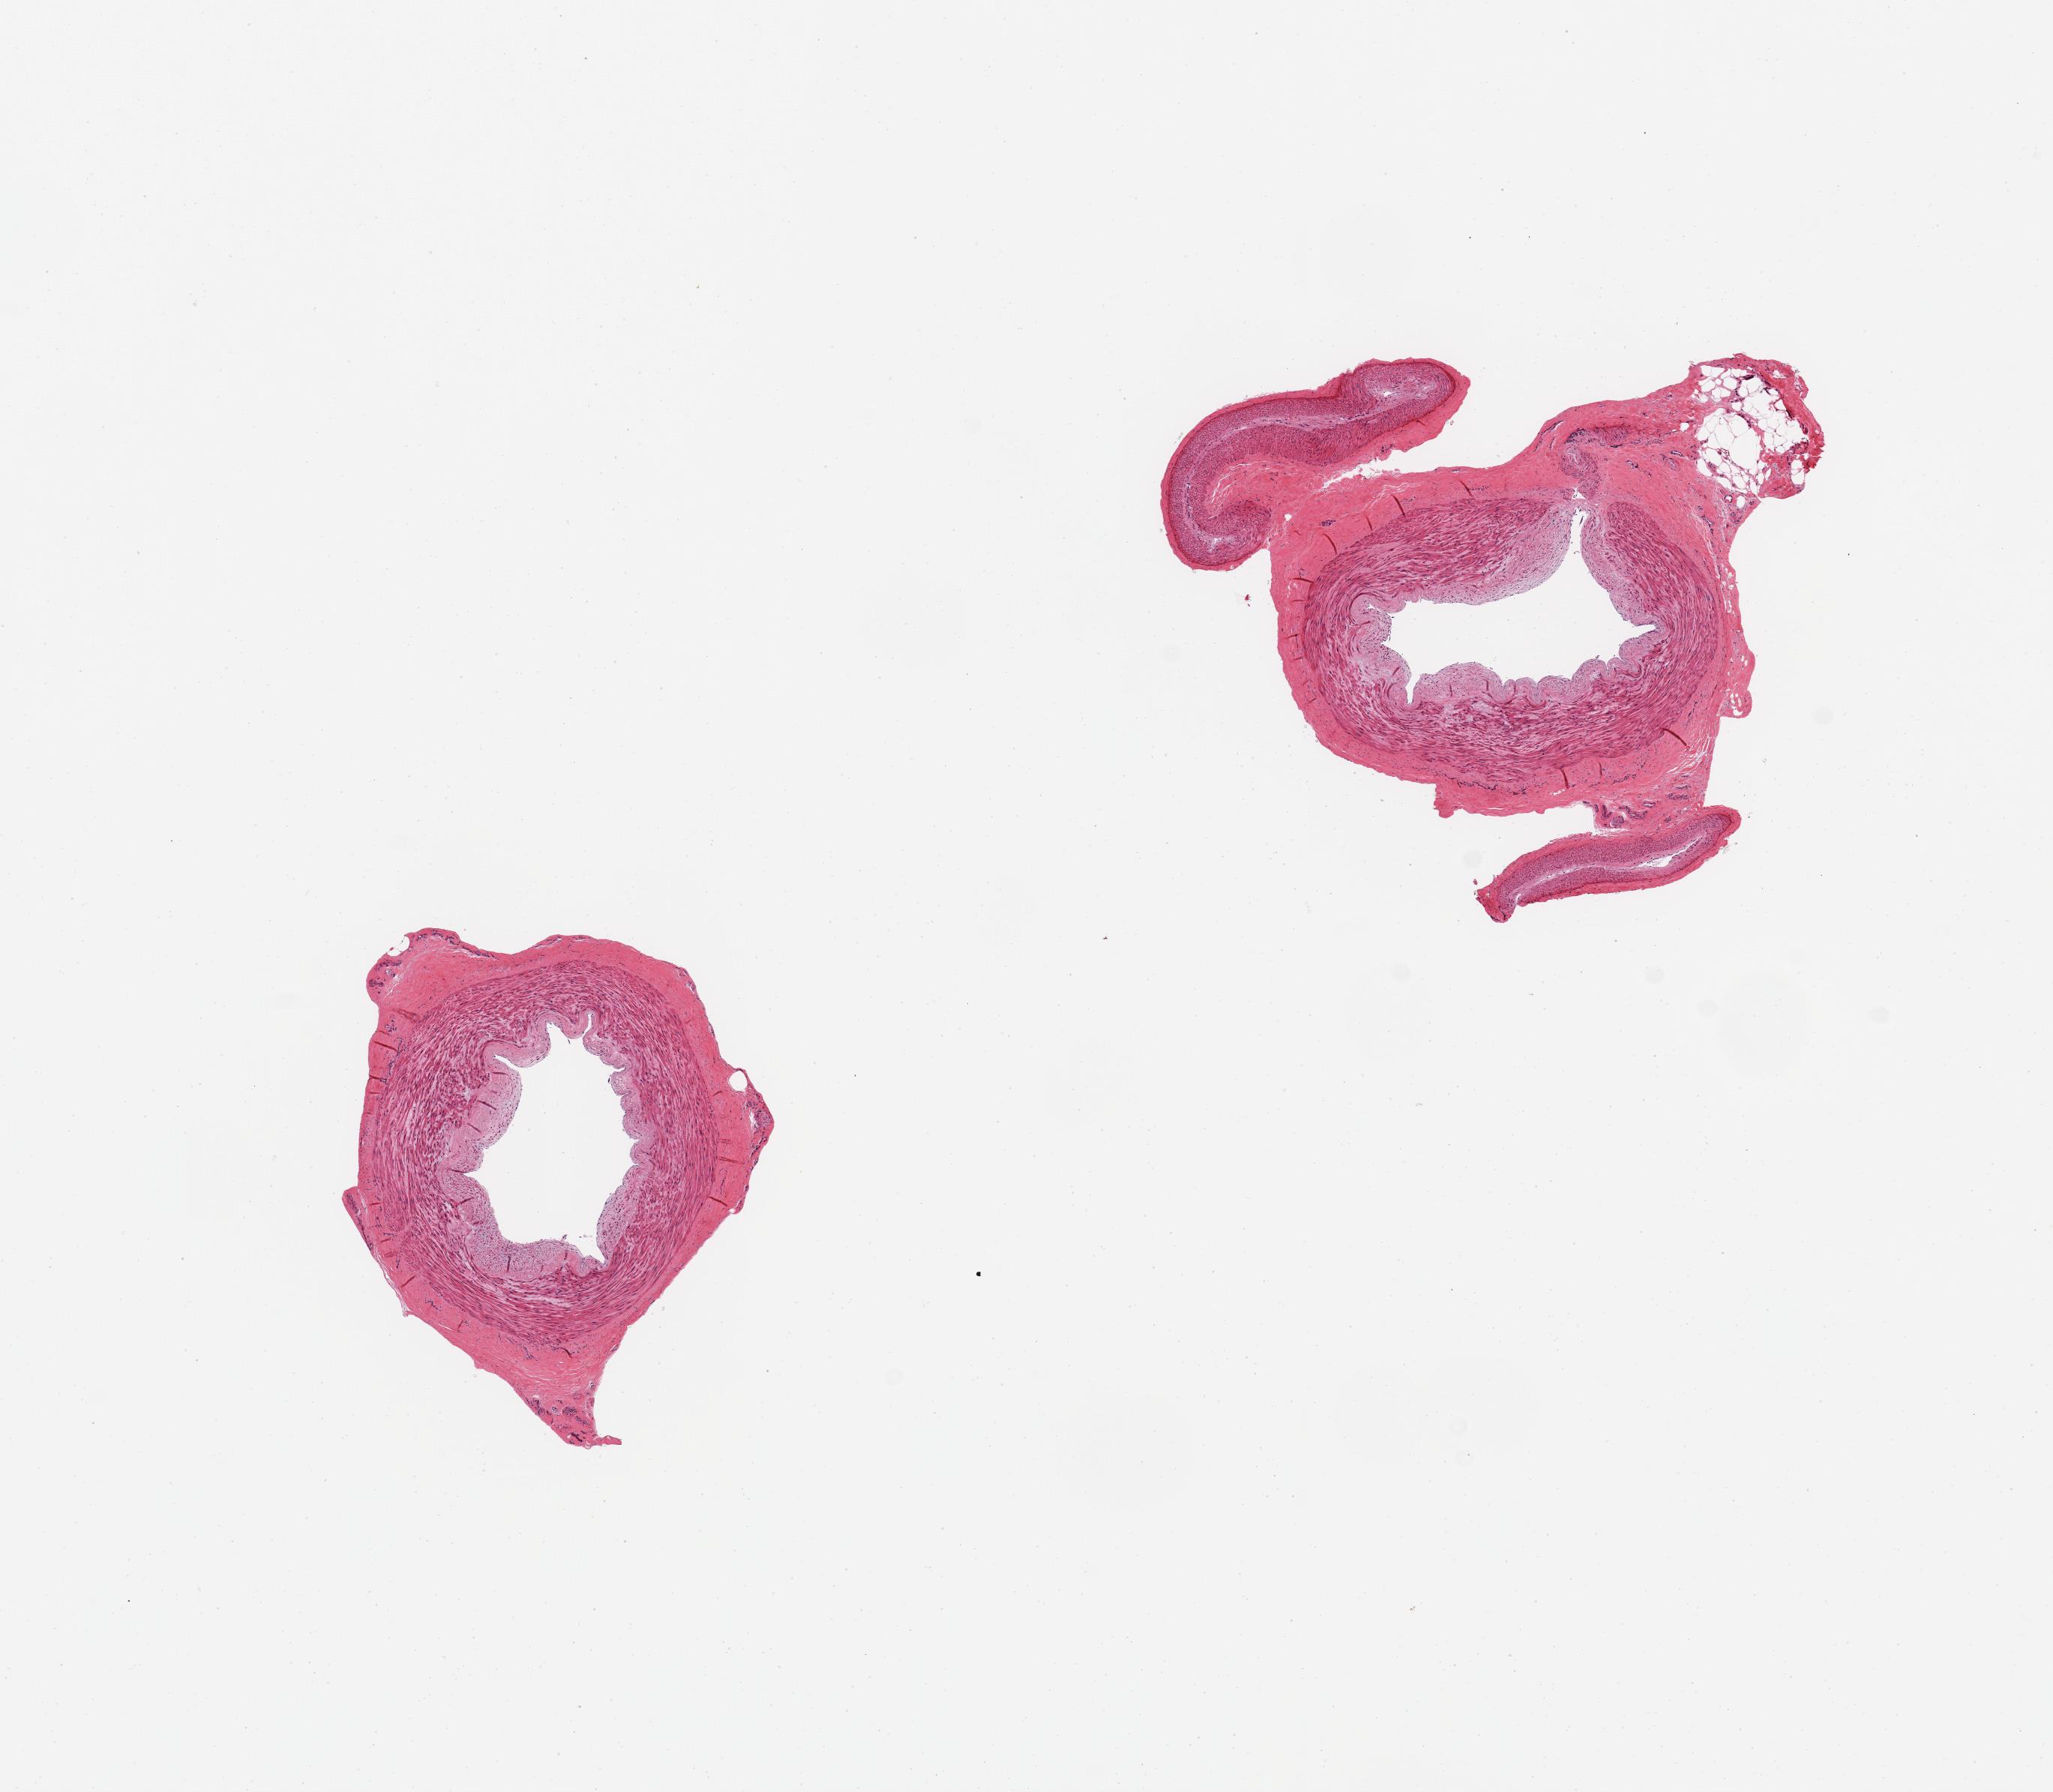
H&E whole-slide image, a low-resolution overview of the entire scanned area, about 10.8 x 9.5 mm (slide scanned at 20x). PAXgene-fixed, paraffin-embedded tissue. Sampled site (target tissue): tibial artery. Donor tissue sample. Donor: male.
- review note (as recorded): 2 pieces; patent vessels; 0.5mm and 1mm attached adventitia